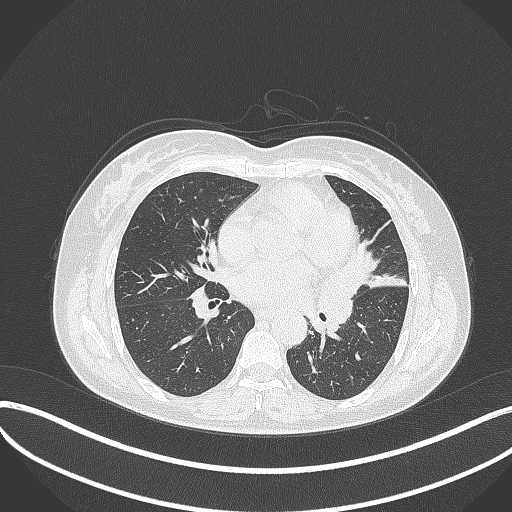
Chest CT, one axial slice. Slice 171 of 373 in the series (ordered by position). 120 kVp. Lung window (W 1500 / L -600 HU). 1 mm slice thickness. 512 × 512 image matrix, field of view 400 × 400 mm. Female patient, age 54 years. Case-level facts recorded for this patient, not image findings: clinical TNM (as recorded): T2a N1 M0; histopathological grade: G3.
Outlined on this slice (rectangle marked by the reading radiologist):
- lung tumour (recorded histology: small cell carcinoma): bounding box (x1, y1, x2, y2) in pixels: (318, 255, 360, 331)